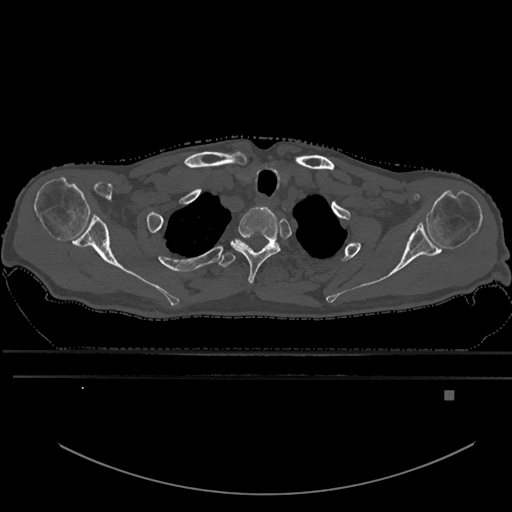
CT including the spine, one axial slice; position 527 of 969 along the scan axis; bone window (W 1800 / L 400 HU); 512 × 512 image matrix. Patient: male, 82 years. Case-level facts recorded for this patient, not image findings: primary cancer: prostate; vertebrae with lytic lesions (as recorded): T11, T9, T8, T2.
Outlined on this slice (semi-automatically segmented with operator editing):
- T1 vertebra: bounding box <231,207,281,285> (left, top, right, bottom; pixels)
- T2 vertebra: <219,239,280,267>